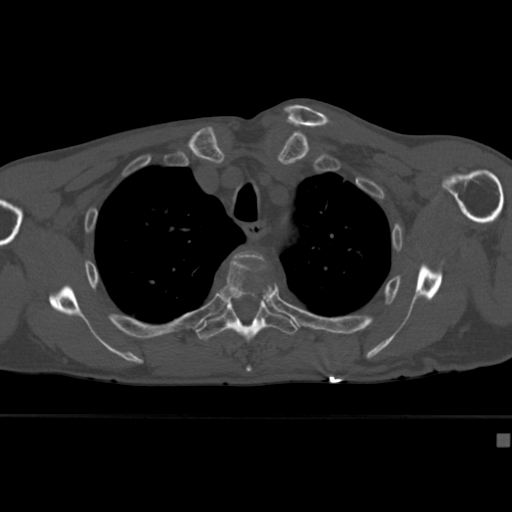
CT including the spine, one axial slice; reconstruction kernel Br40s; 120 kVp; bone window (W 1800 / L 400 HU); 1.5 mm slice thickness; 512 × 512 image matrix, field of view 337 × 337 mm. Male patient, age 64 years. Case-level facts recorded for this patient, not image findings: primary cancer: uterus.
Outlined on this slice (semi-automatically segmented with operator editing):
- T3 vertebra: bounding box [x1, y1, x2, y2] px = [234, 251, 263, 259]
- T4 vertebra: [219, 257, 278, 372]
- T5 vertebra: [196, 297, 299, 345]